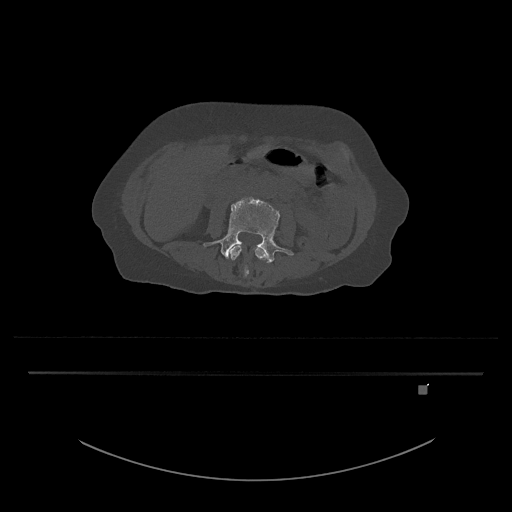
CT including the spine, one axial slice; slice 383 of 797 in the series (ordered by position); reconstruction kernel Br40s/3; bone window (W 1800 / L 400 HU); 0.5 mm slice thickness; 512 × 512 image matrix, field of view 500 × 500 mm. Female patient, age 57 years. Case-level facts recorded for this patient, not image findings: primary cancer: cervical.
Annotated regions visible in this slice (semi-automatically segmented with operator editing):
- L3 vertebra: bounding box [x1, y1, x2, y2] px = [230, 245, 267, 276]
- L4 vertebra: [203, 197, 294, 264]